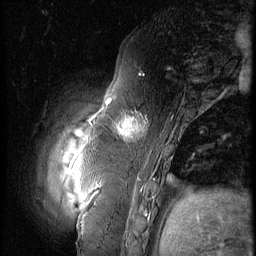
Breast MRI (dynamic contrast-enhanced), one sagittal slice; position 9 of 60 along the scan axis; 3 images stored at this slice position (order not interpretable as contrast timing); 1.5 T; TE 4.2 ms, TR 9 ms; 256 × 256 image matrix. Female patient, age 57 years. From the clinical record (not read from this slice): setting: breast cancer imaged before/during neoadjuvant chemotherapy; receptor status: triple-negative.
Outlined on this slice (semi-automatically segmented with operator editing):
- analysis volume of interest (the breast-tissue region the enhancement analysis was run in; not a lesion): bounding box (x1, y1, x2, y2) in pixels: (106, 101, 157, 152)
- tumour enhancement mask (voxels above the 140 % enhancement threshold inside the analysis volume of interest): (107, 101, 142, 135)